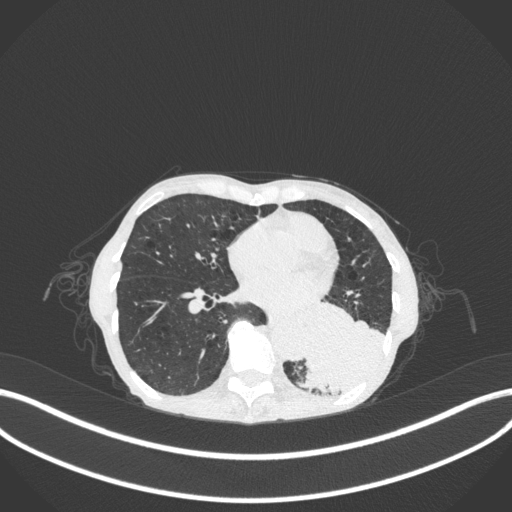
Chest CT, one axial slice. 120 kVp. Lung window (W 1500 / L -600 HU). 1 mm slice thickness. 512 × 512 image matrix, field of view 400 × 400 mm. Female patient, age 70 years. Case-level facts recorded for this patient, not image findings: clinical TNM (as recorded): T3 N0 M0.
Structures marked on this image (rectangle marked by the reading radiologist):
- lung tumour (recorded histology: small cell carcinoma): box from (x=301, y=289) to (x=388, y=399) px